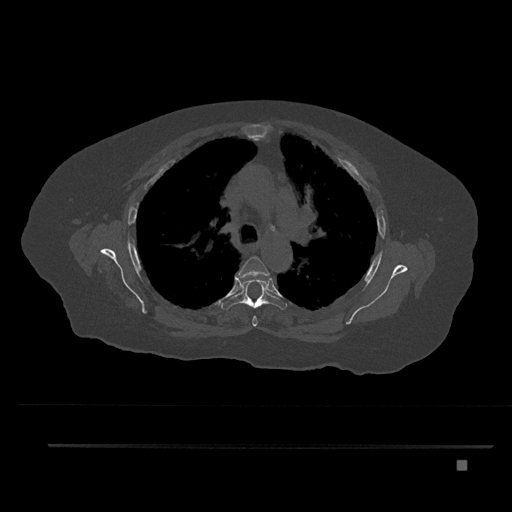
CT including the spine, one axial slice. Slice 579 of 797 in the series (ordered by position). Reconstruction kernel Br40s/3. Bone window (W 1800 / L 400 HU). 0.5 mm slice thickness. 512 × 512 image matrix, field of view 437 × 437 mm. Female patient, age 76 years. Case-level facts recorded for this patient, not image findings: primary cancer: lung.
Annotated regions visible in this slice (semi-automatically segmented with operator editing):
- T4 vertebra: bounding box [x1, y1, x2, y2] px = [236, 256, 269, 327]
- T5 vertebra: [220, 278, 287, 310]